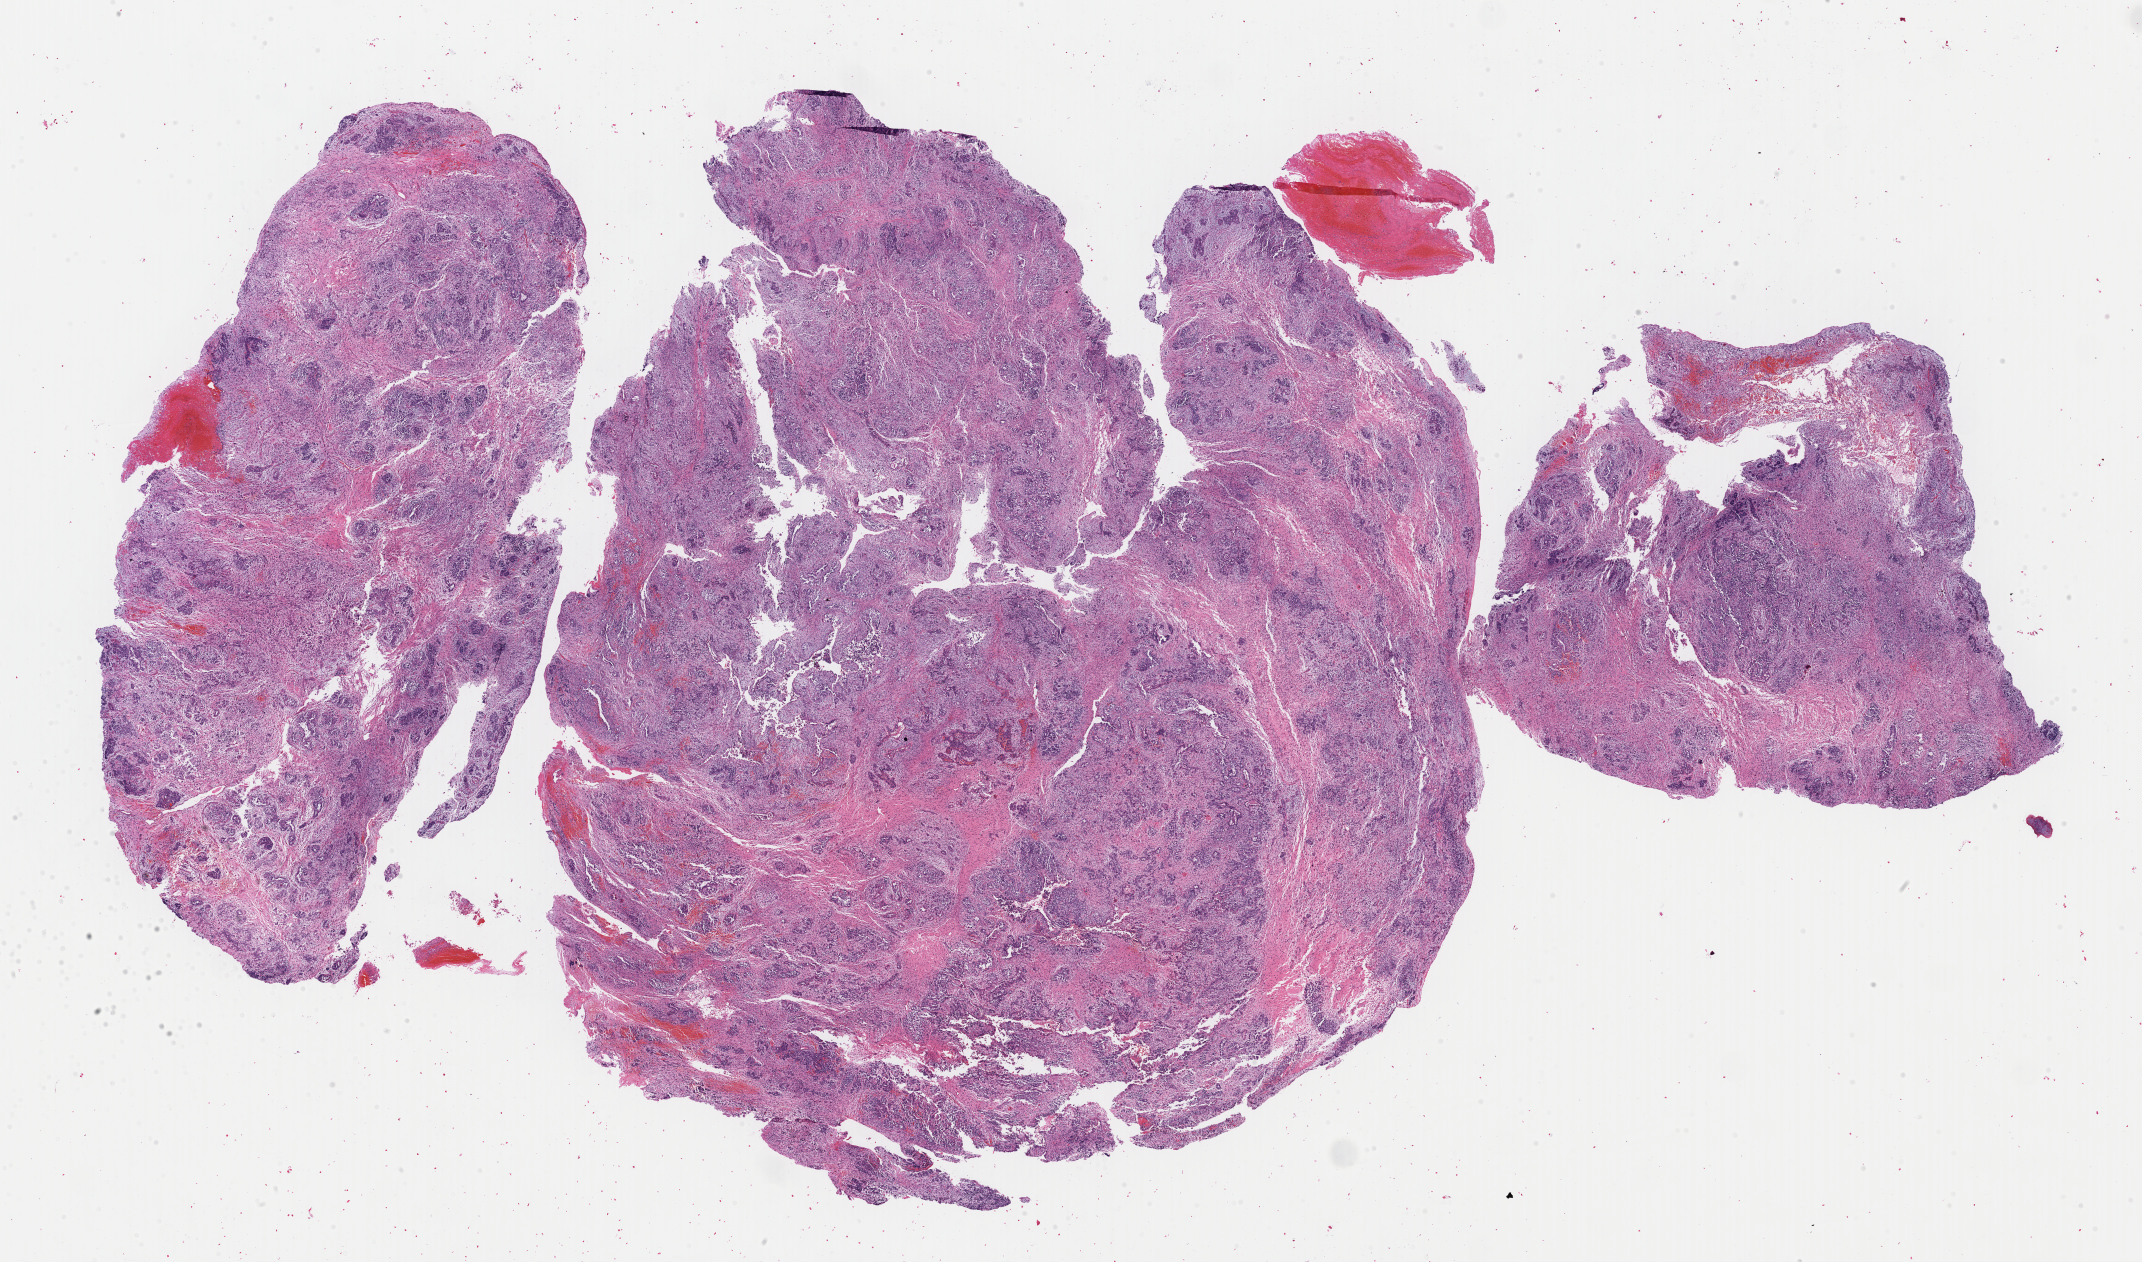
Digitized Hematoxylin and eosin (H&E) stained tissue section (whole slide), low-resolution overview of the scanned area, about 33.8 x 19.9 mm (slide scanned at 40x). Formalin-fixed paraffin-embedded (FFPE) diagnostic section. Uterus, primary tumour sample. Female patient; age at initial diagnosis 62 years.
Pathologic diagnosis: Mesodermal mixed tumor. FIGO stage: III.